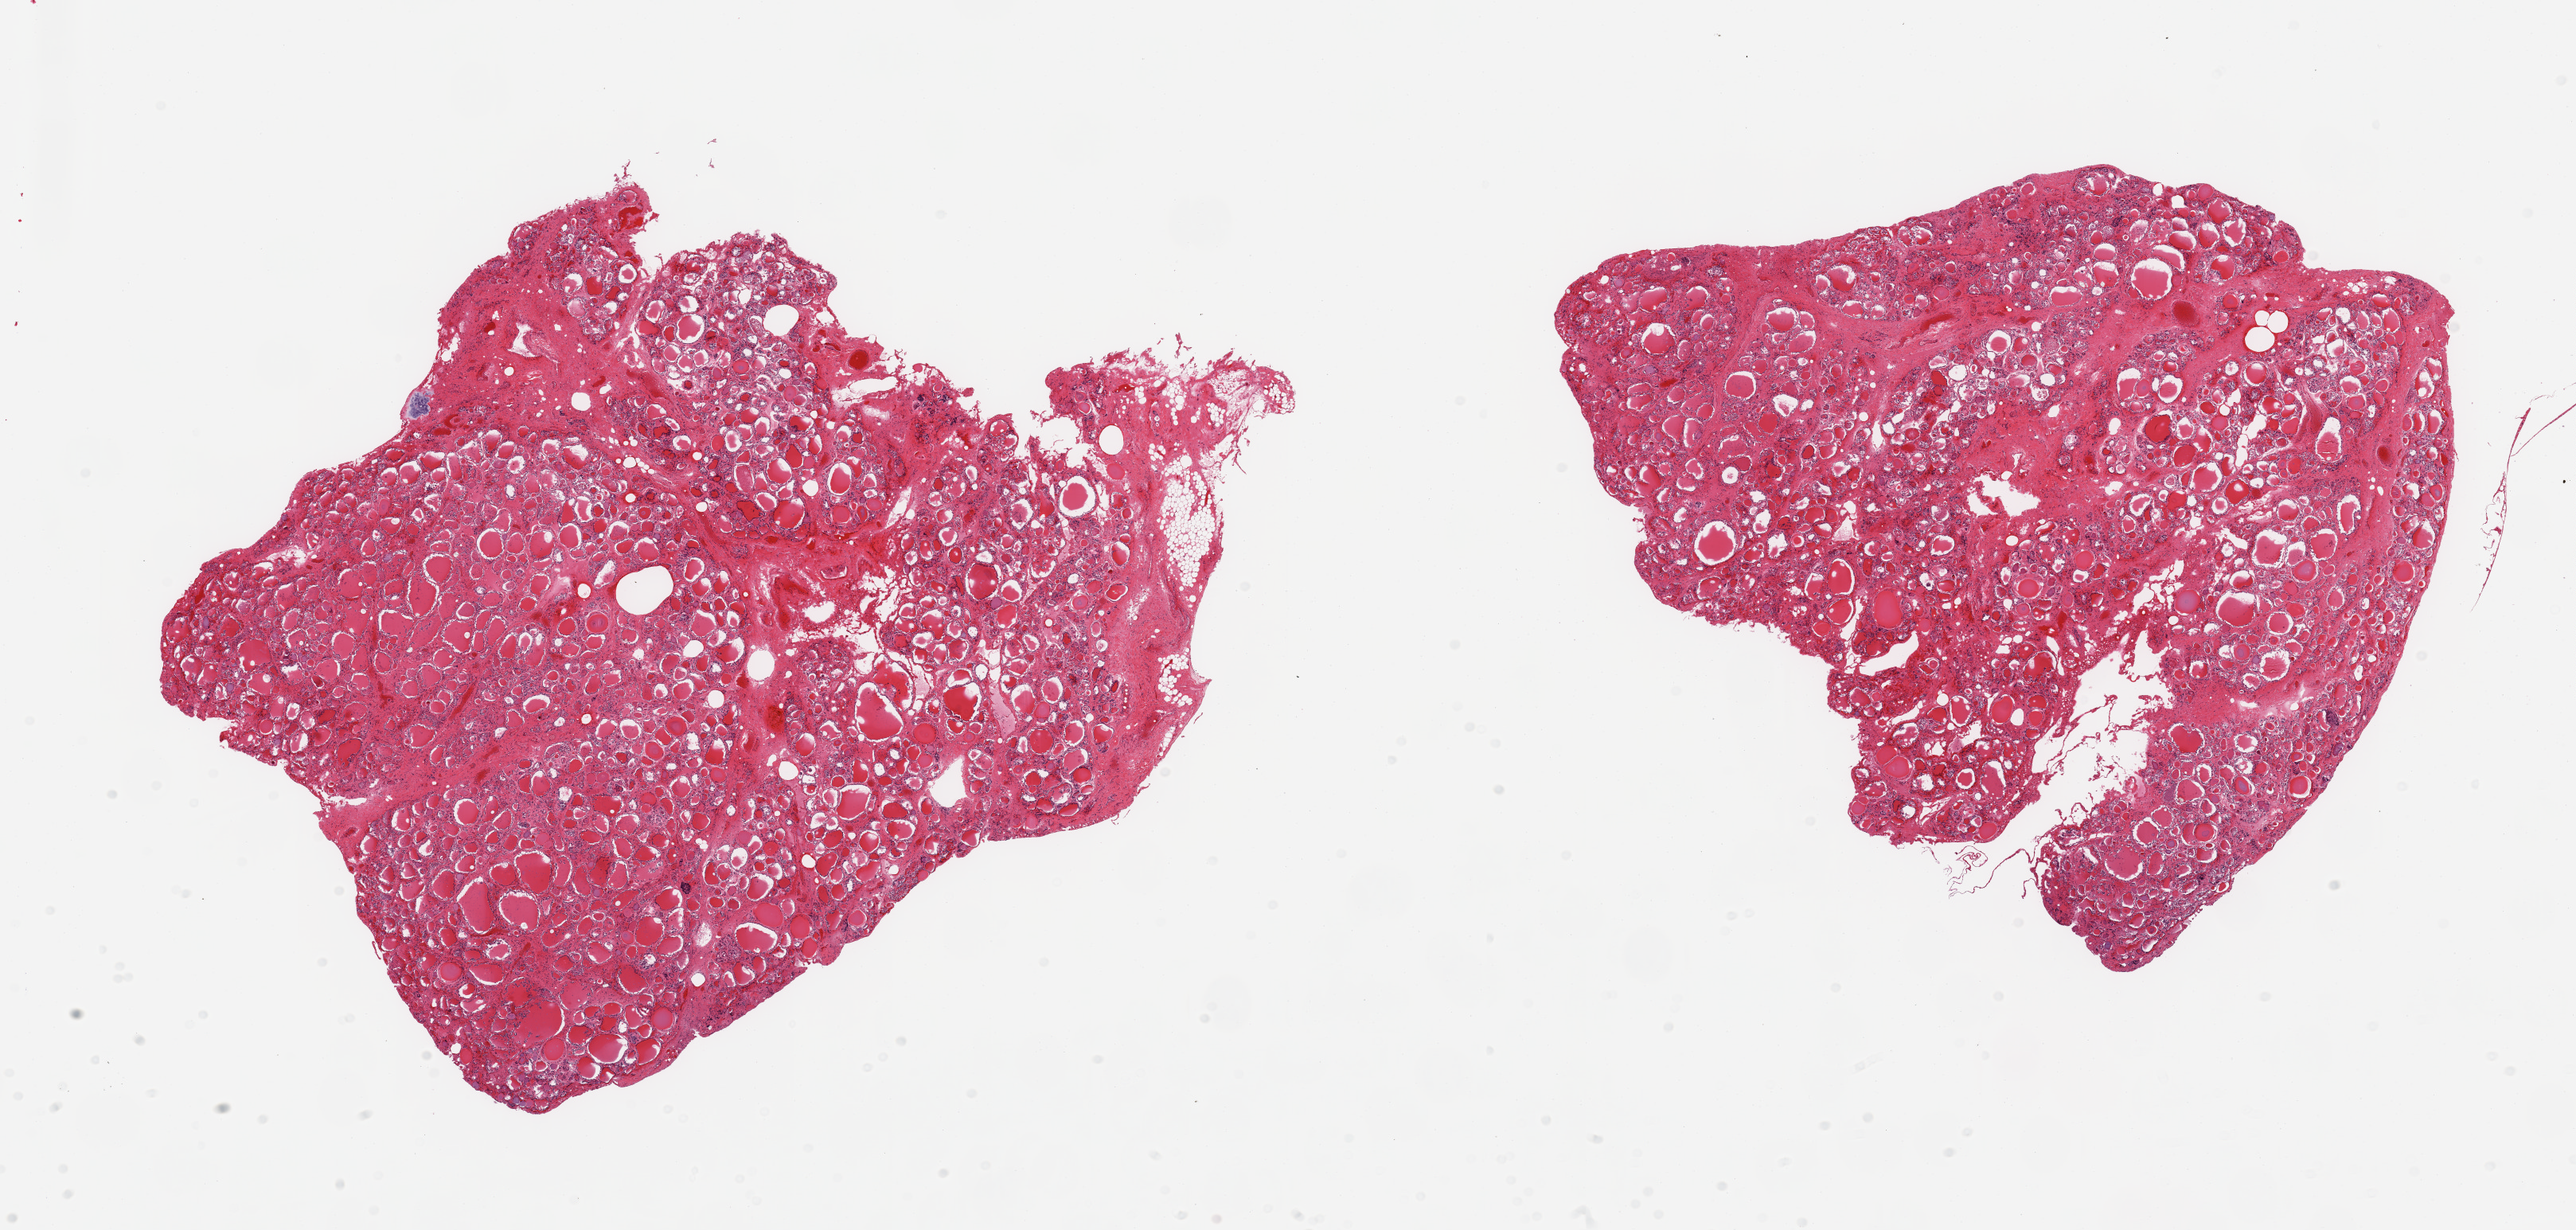
Digitized hematoxylin and eosin (H&E)-stained section, brightfield, shown as a low-resolution overview of the whole scanned area (about 25.6 x 12.2 mm), PAXgene-fixed paraffin-embedded (PFPE) section, section of thyroid (target tissue), donor tissue sample.
* pathologist's review note for this sample: 2 pieces, regressive changes, nodeular goiter